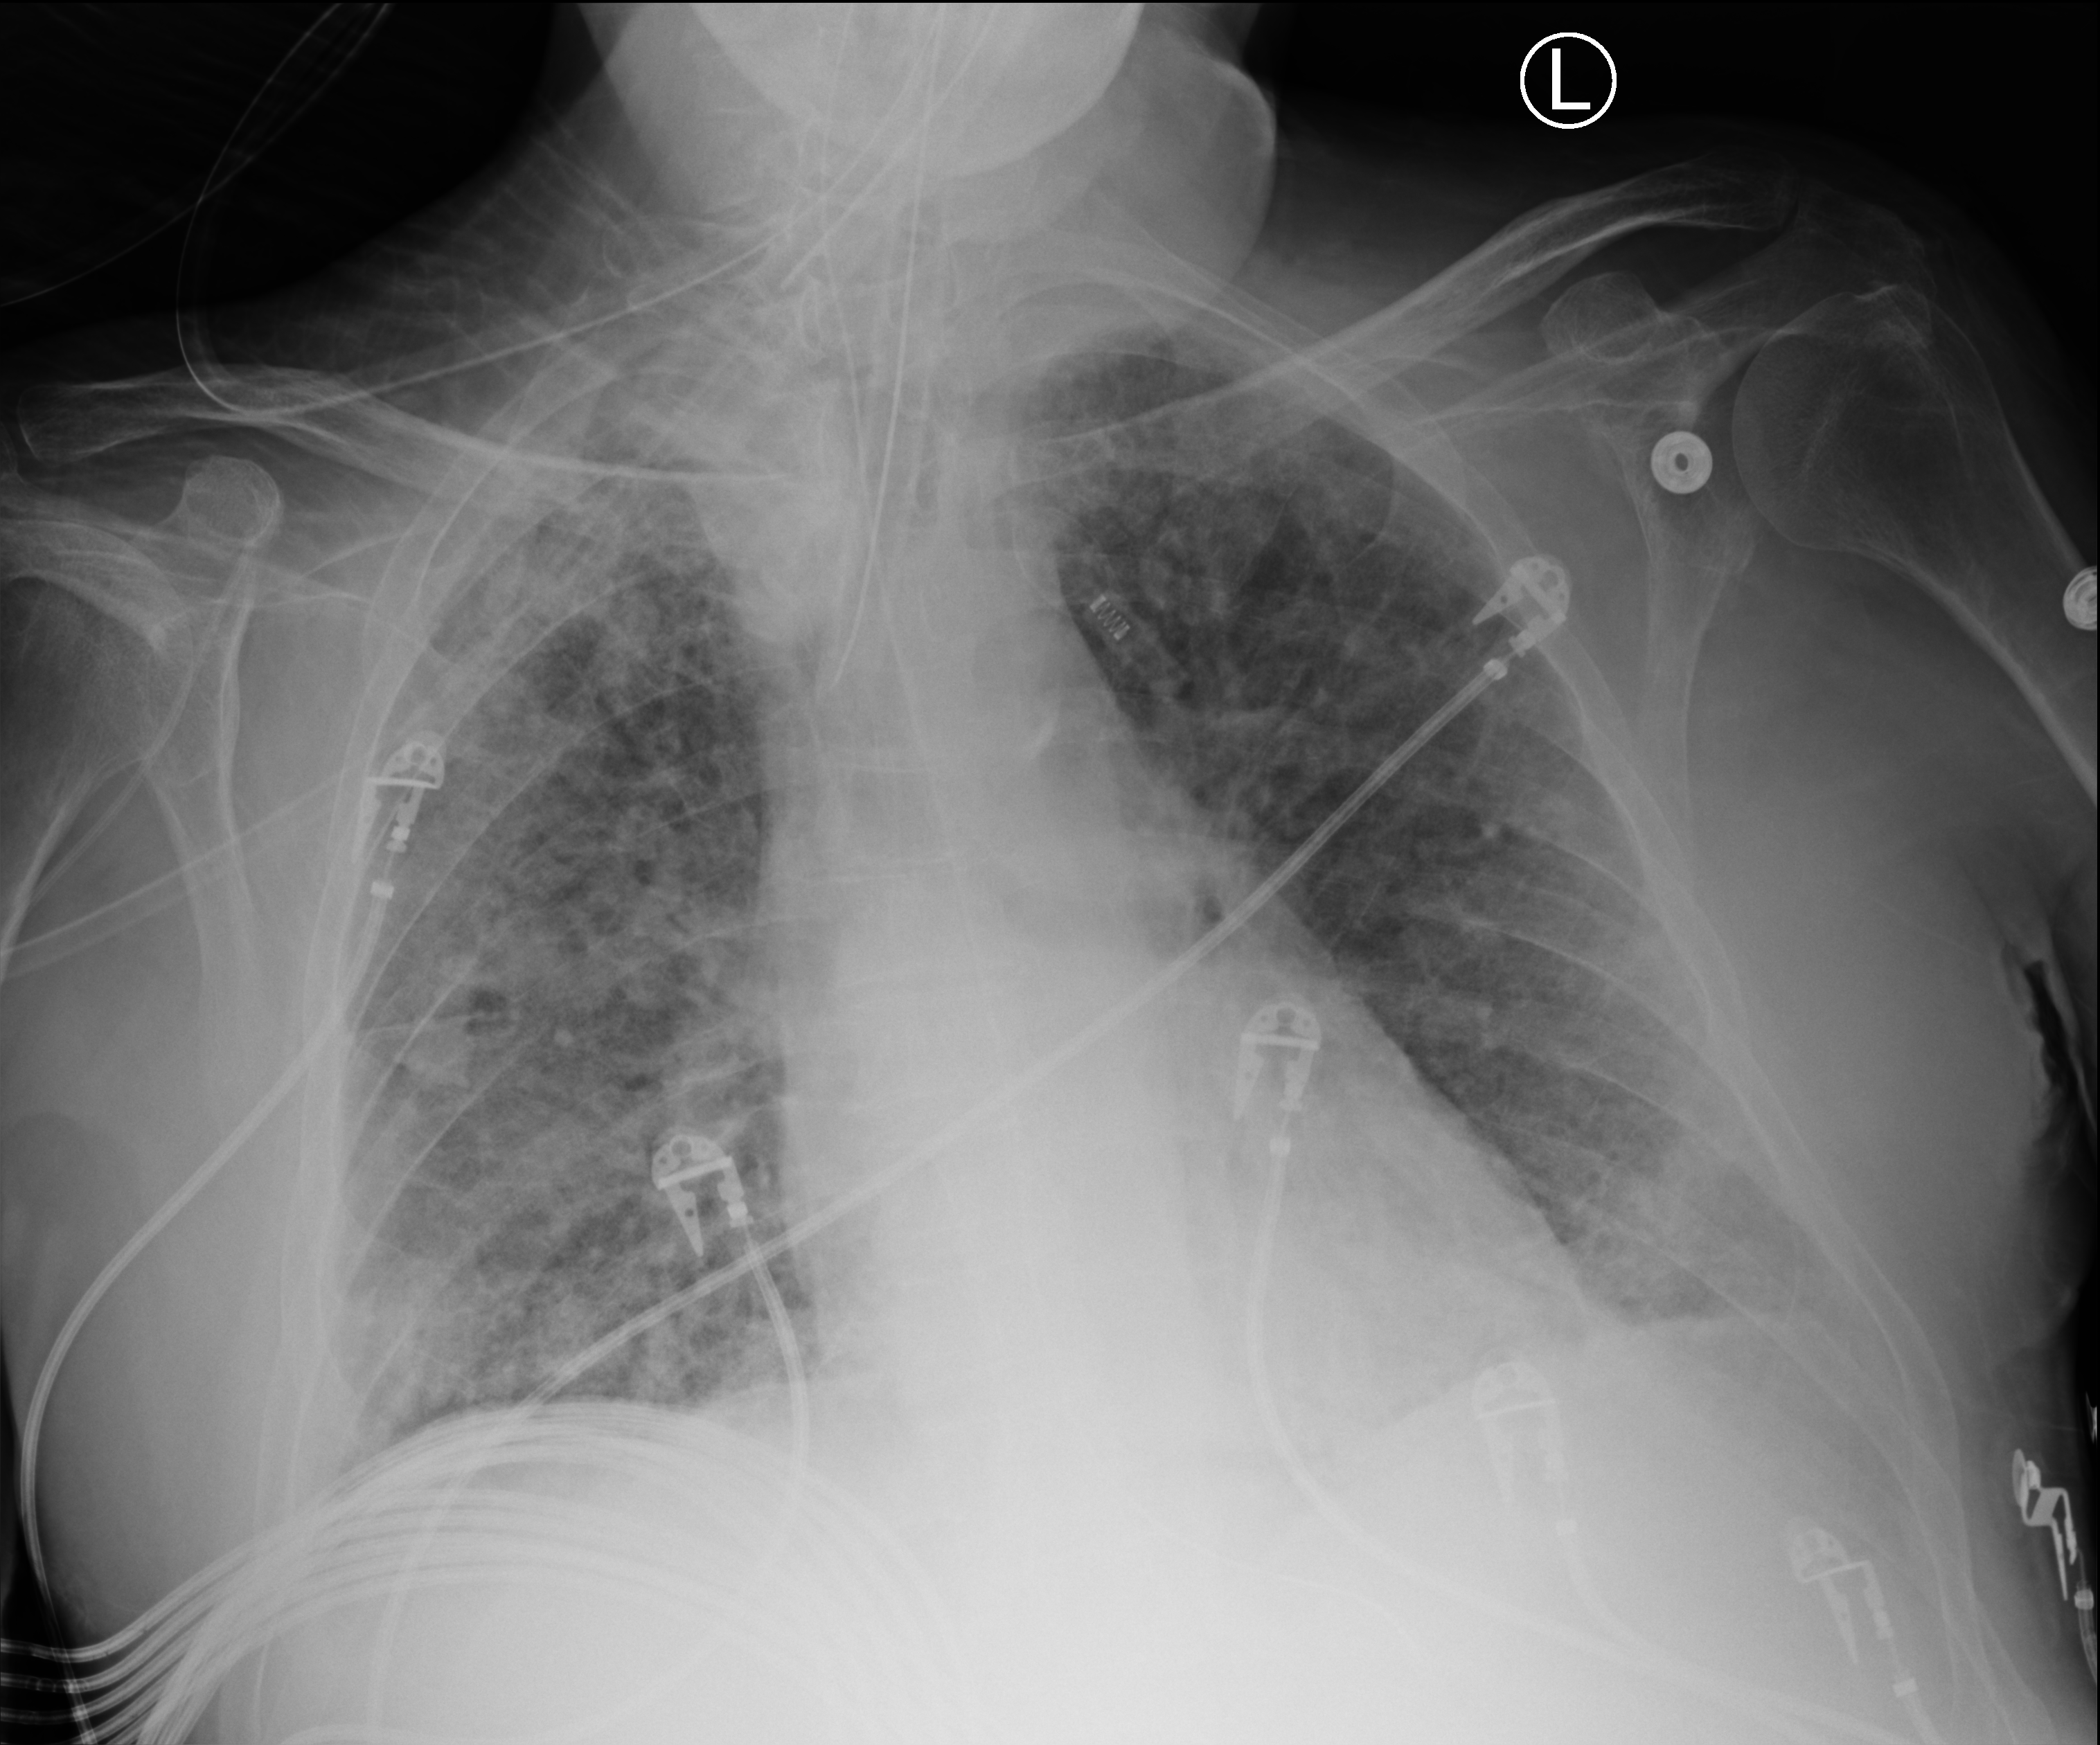
Portable chest radiograph, anteroposterior (AP) projection. Patient hospitalised with COVID-19; male, aged 60–74 years.
From the hospital-stay record, not from the radiograph (when in the stay this image was taken is not recorded):
- other chronic lung disease (admission record): no
- COPD (admission record): no